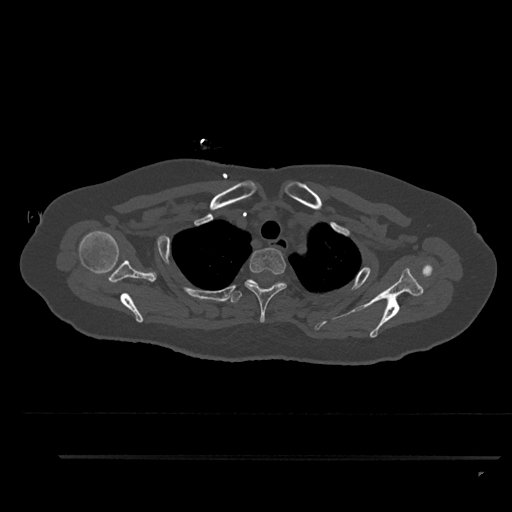
CT including the spine, one axial slice. Slice 713 of 797 in the series (ordered by position). Reconstruction kernel Br40s/3. 120 kVp. Bone window (W 1800 / L 400 HU). 0.5 mm slice thickness. 512 × 512 image matrix, field of view 408 × 408 mm. Patient: female, 44 years. From the clinical record (not read from this slice): primary cancer: renal; vertebrae with lytic lesions (as recorded): L1.
Outlined on this slice (semi-automatic segmentation, software-assisted and operator-edited):
- T1 vertebra: bounding box (x1, y1, x2, y2) in pixels: (272, 282, 285, 287)
- T2 vertebra: (245, 248, 287, 322)
- T3 vertebra: (229, 279, 283, 303)